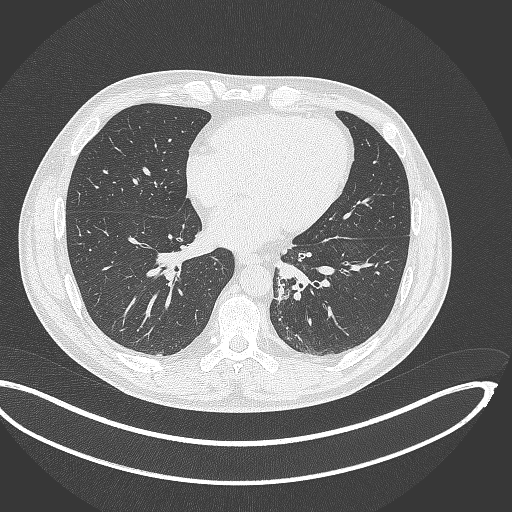
Chest CT, one axial slice; slice 136 of 362 in the series (ordered by position); reconstruction kernel B70f; 120 kVp; lung window (W 1500 / L -600 HU); 1 mm slice thickness; 512 × 512 image matrix, field of view 442 × 442 mm. Patient: male, 50 years. From the clinical record (not read from this slice): clinical TNM (as recorded): T2a N3 M0.
Outlined on this slice (rectangle marked by the reading radiologist):
- lung tumour (recorded histology: squamous cell carcinoma): bounding box [x1, y1, x2, y2] px = [271, 279, 292, 304]